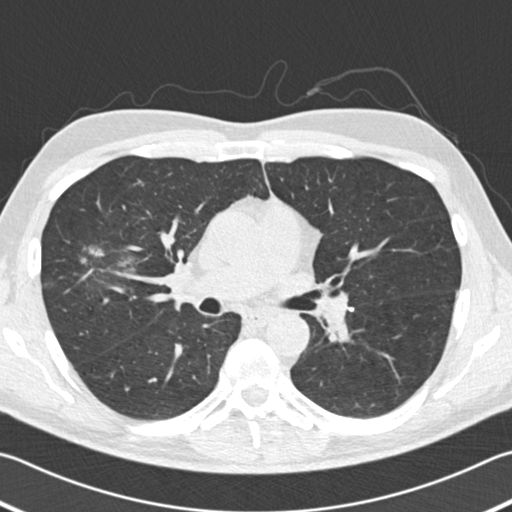
Low-dose screening chest CT, one axial slice; position 110 of 182 along the scan axis; reconstruction kernel B30f; lung window (W 1500 / L -600 HU); 2 mm slice thickness; 512 × 512 image matrix, field of view 344 × 344 mm.
Annotated regions visible in this slice (outlined manually by an expert reader):
- lesion 1 (tumor, upper lobe of right lung): bounding box [x1, y1, x2, y2] px = [80, 244, 107, 263]